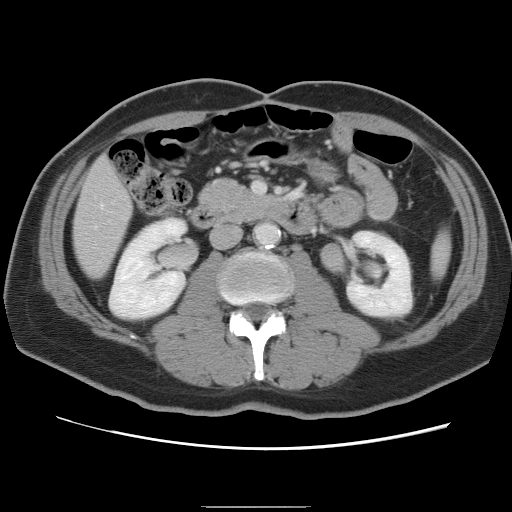
Contrast-enhanced abdominal CT, one axial slice; slice 25 of 87 in the series (ordered by position); intravenous contrast given; soft-tissue window (W 400 / L 40 HU); 5 mm slice thickness; 512 × 512 image matrix, field of view 363 × 363 mm. Male patient, age 63 years. Case-level facts recorded for this patient, not image findings: diagnosis: colorectal cancer liver metastases, imaged before liver resection; multiple liver metastases: no; largest metastasis: 9 cm; disease in both lobes: no.
Annotated regions visible in this slice (expert manual segmentation):
- liver: bounding box <74,159,132,277> (left, top, right, bottom; pixels)
- planned liver remnant (the part of the liver to remain after resection): <74,158,132,277>